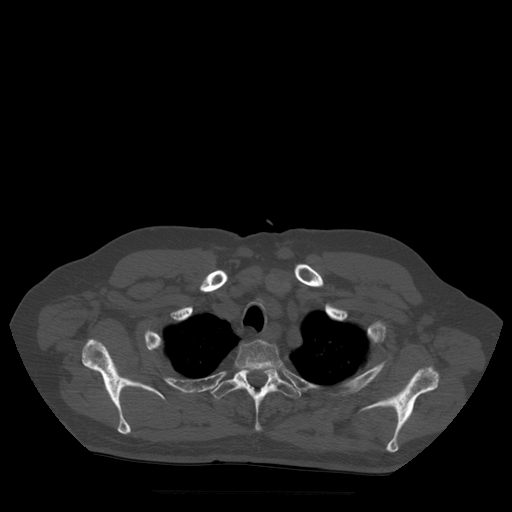
CT including the spine, one axial slice; position 415 of 522 along the scan axis; bone window (W 1800 / L 400 HU); 1.25 mm slice thickness; 512 × 512 image matrix, field of view 420 × 420 mm. Patient age 72 years. Case-level facts recorded for this patient, not image findings: primary cancer: prostate.
Structures marked on this image (semi-automatically segmented with operator editing):
- T2 vertebra: box from (x=236, y=340) to (x=281, y=374) px
- T3 vertebra: (x=211, y=366)–(x=302, y=432)